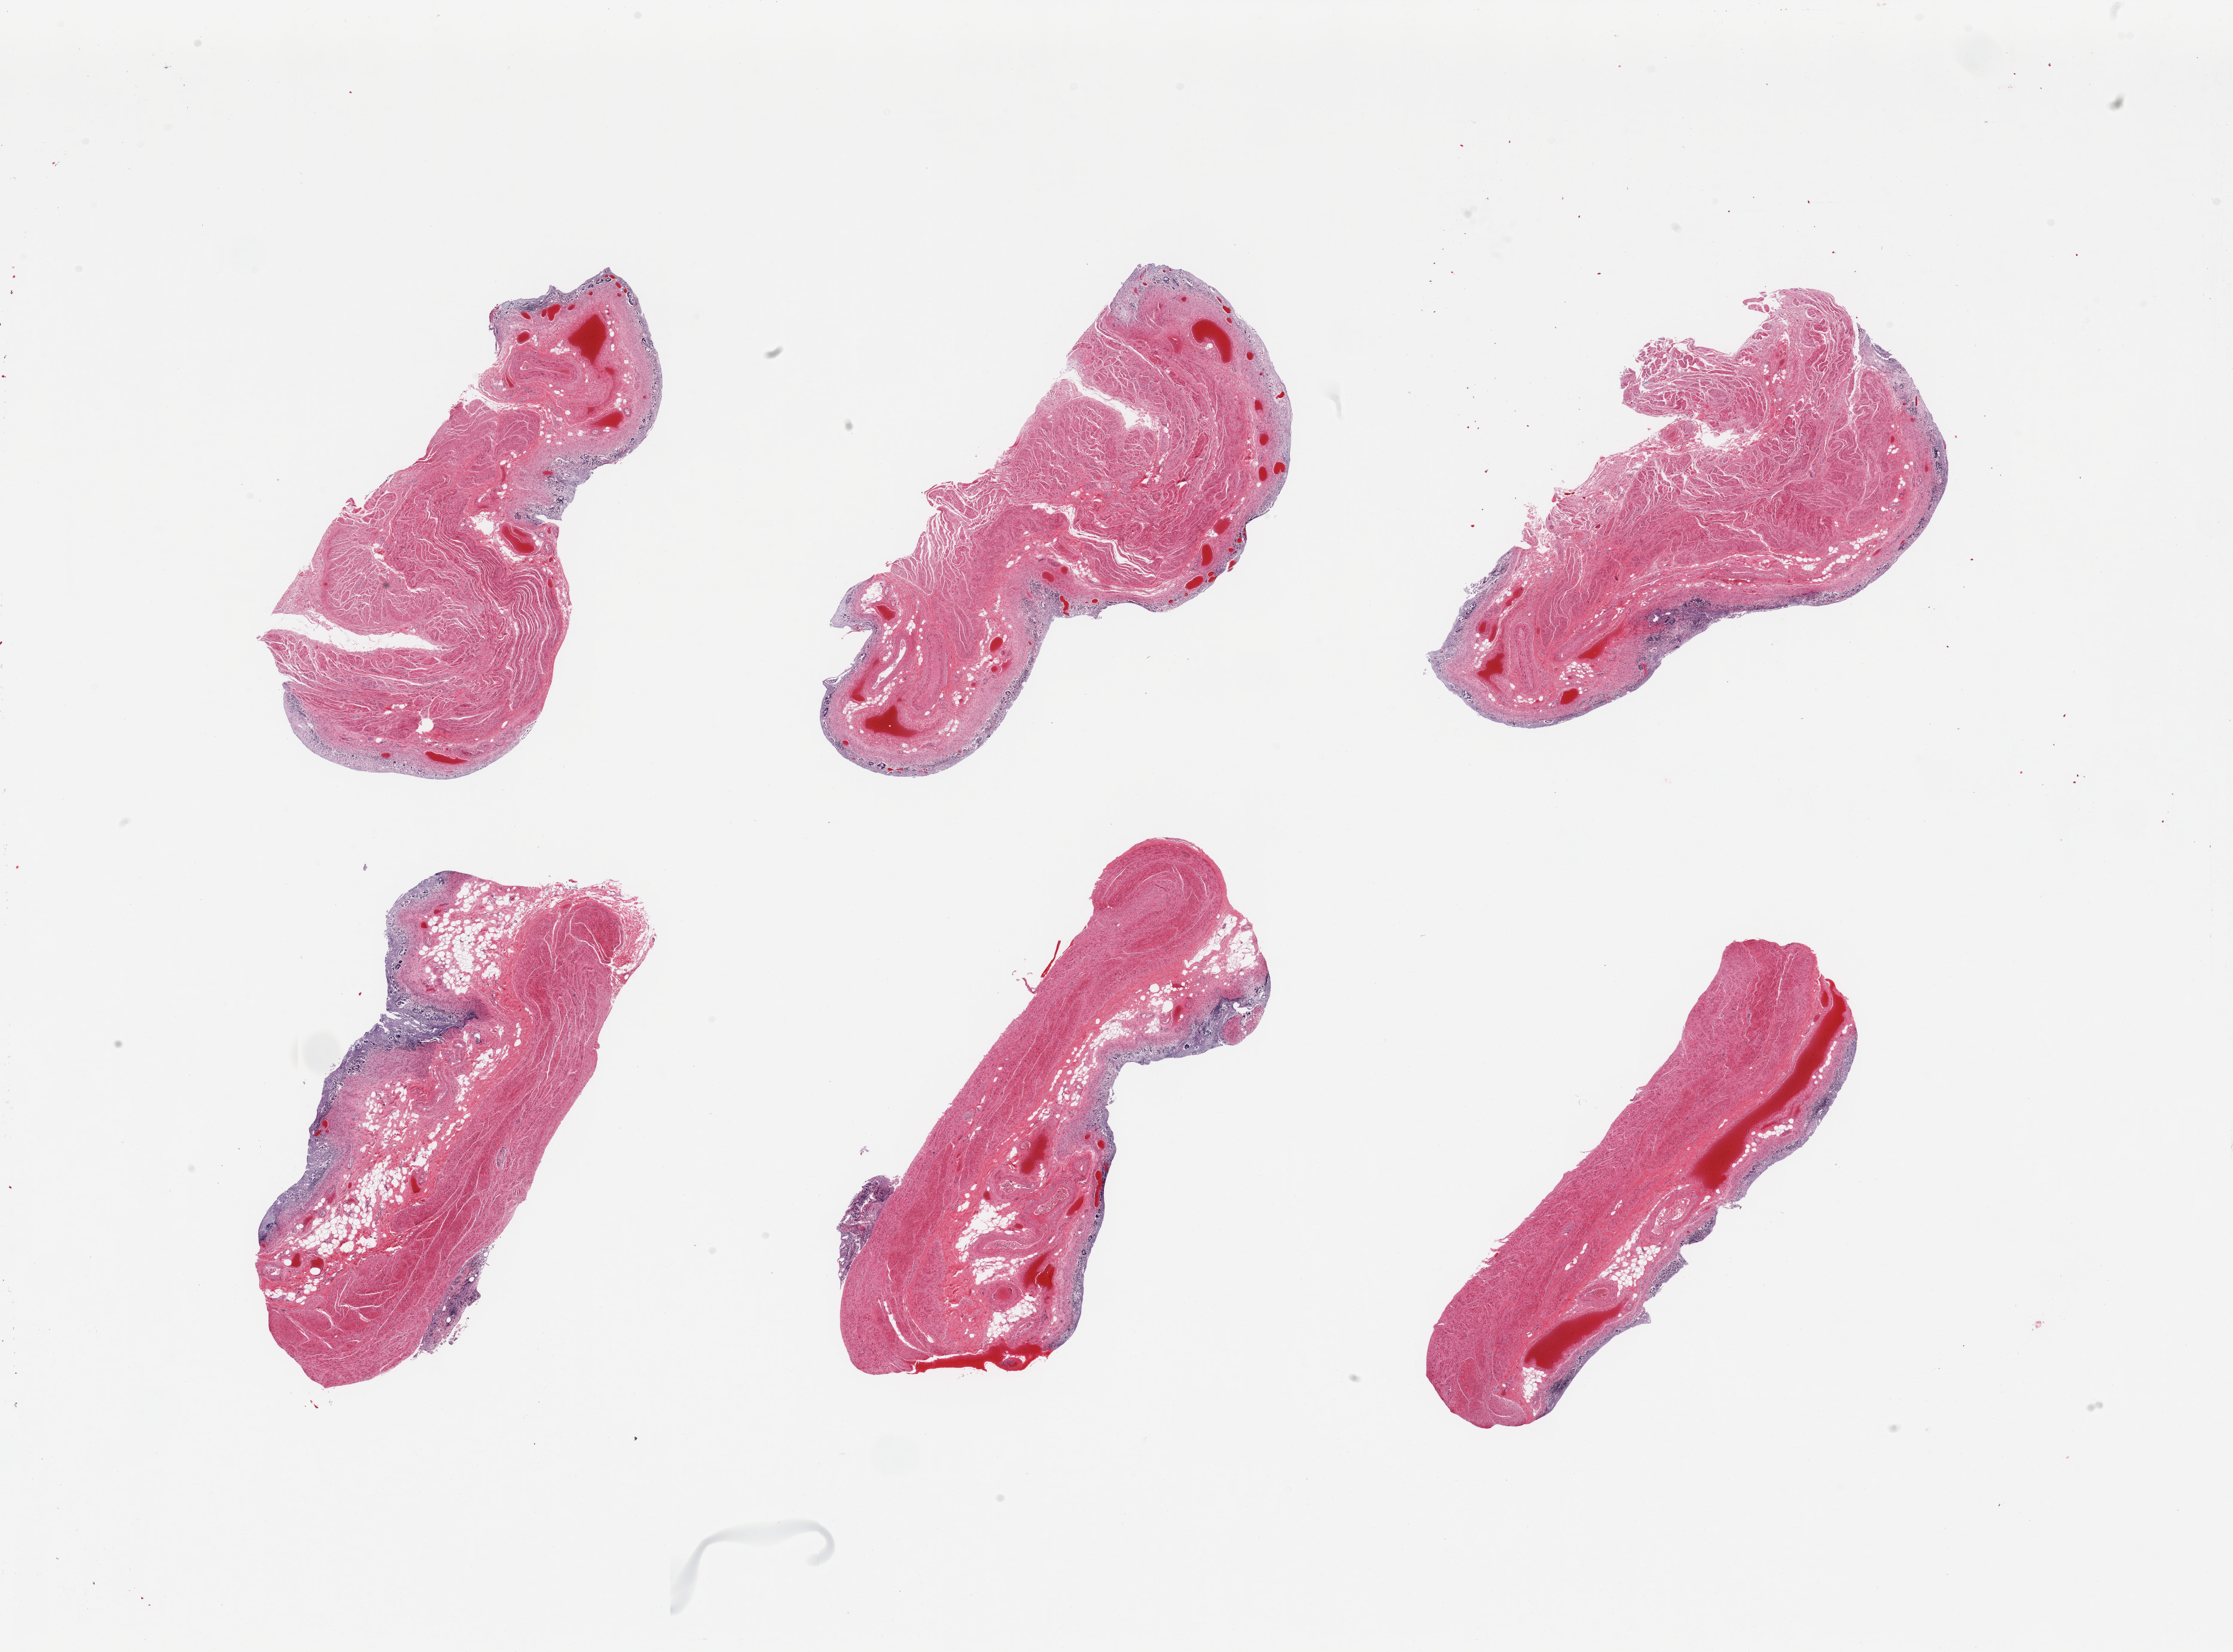
Digitized hematoxylin and eosin (H&E)-stained section — a low-resolution overview of the entire scanned area, about 29.5 x 21.9 mm (from a 20x scan), PAXgene-fixed paraffin-embedded (PFPE) section, target tissue: stomach, donor tissue sample. Donor sex: female.
Pathologist's review note for this sample: 6 pieces, target mucosa 0.1-0.2mm, partly sloughing, glandular elements totally autolyzed.